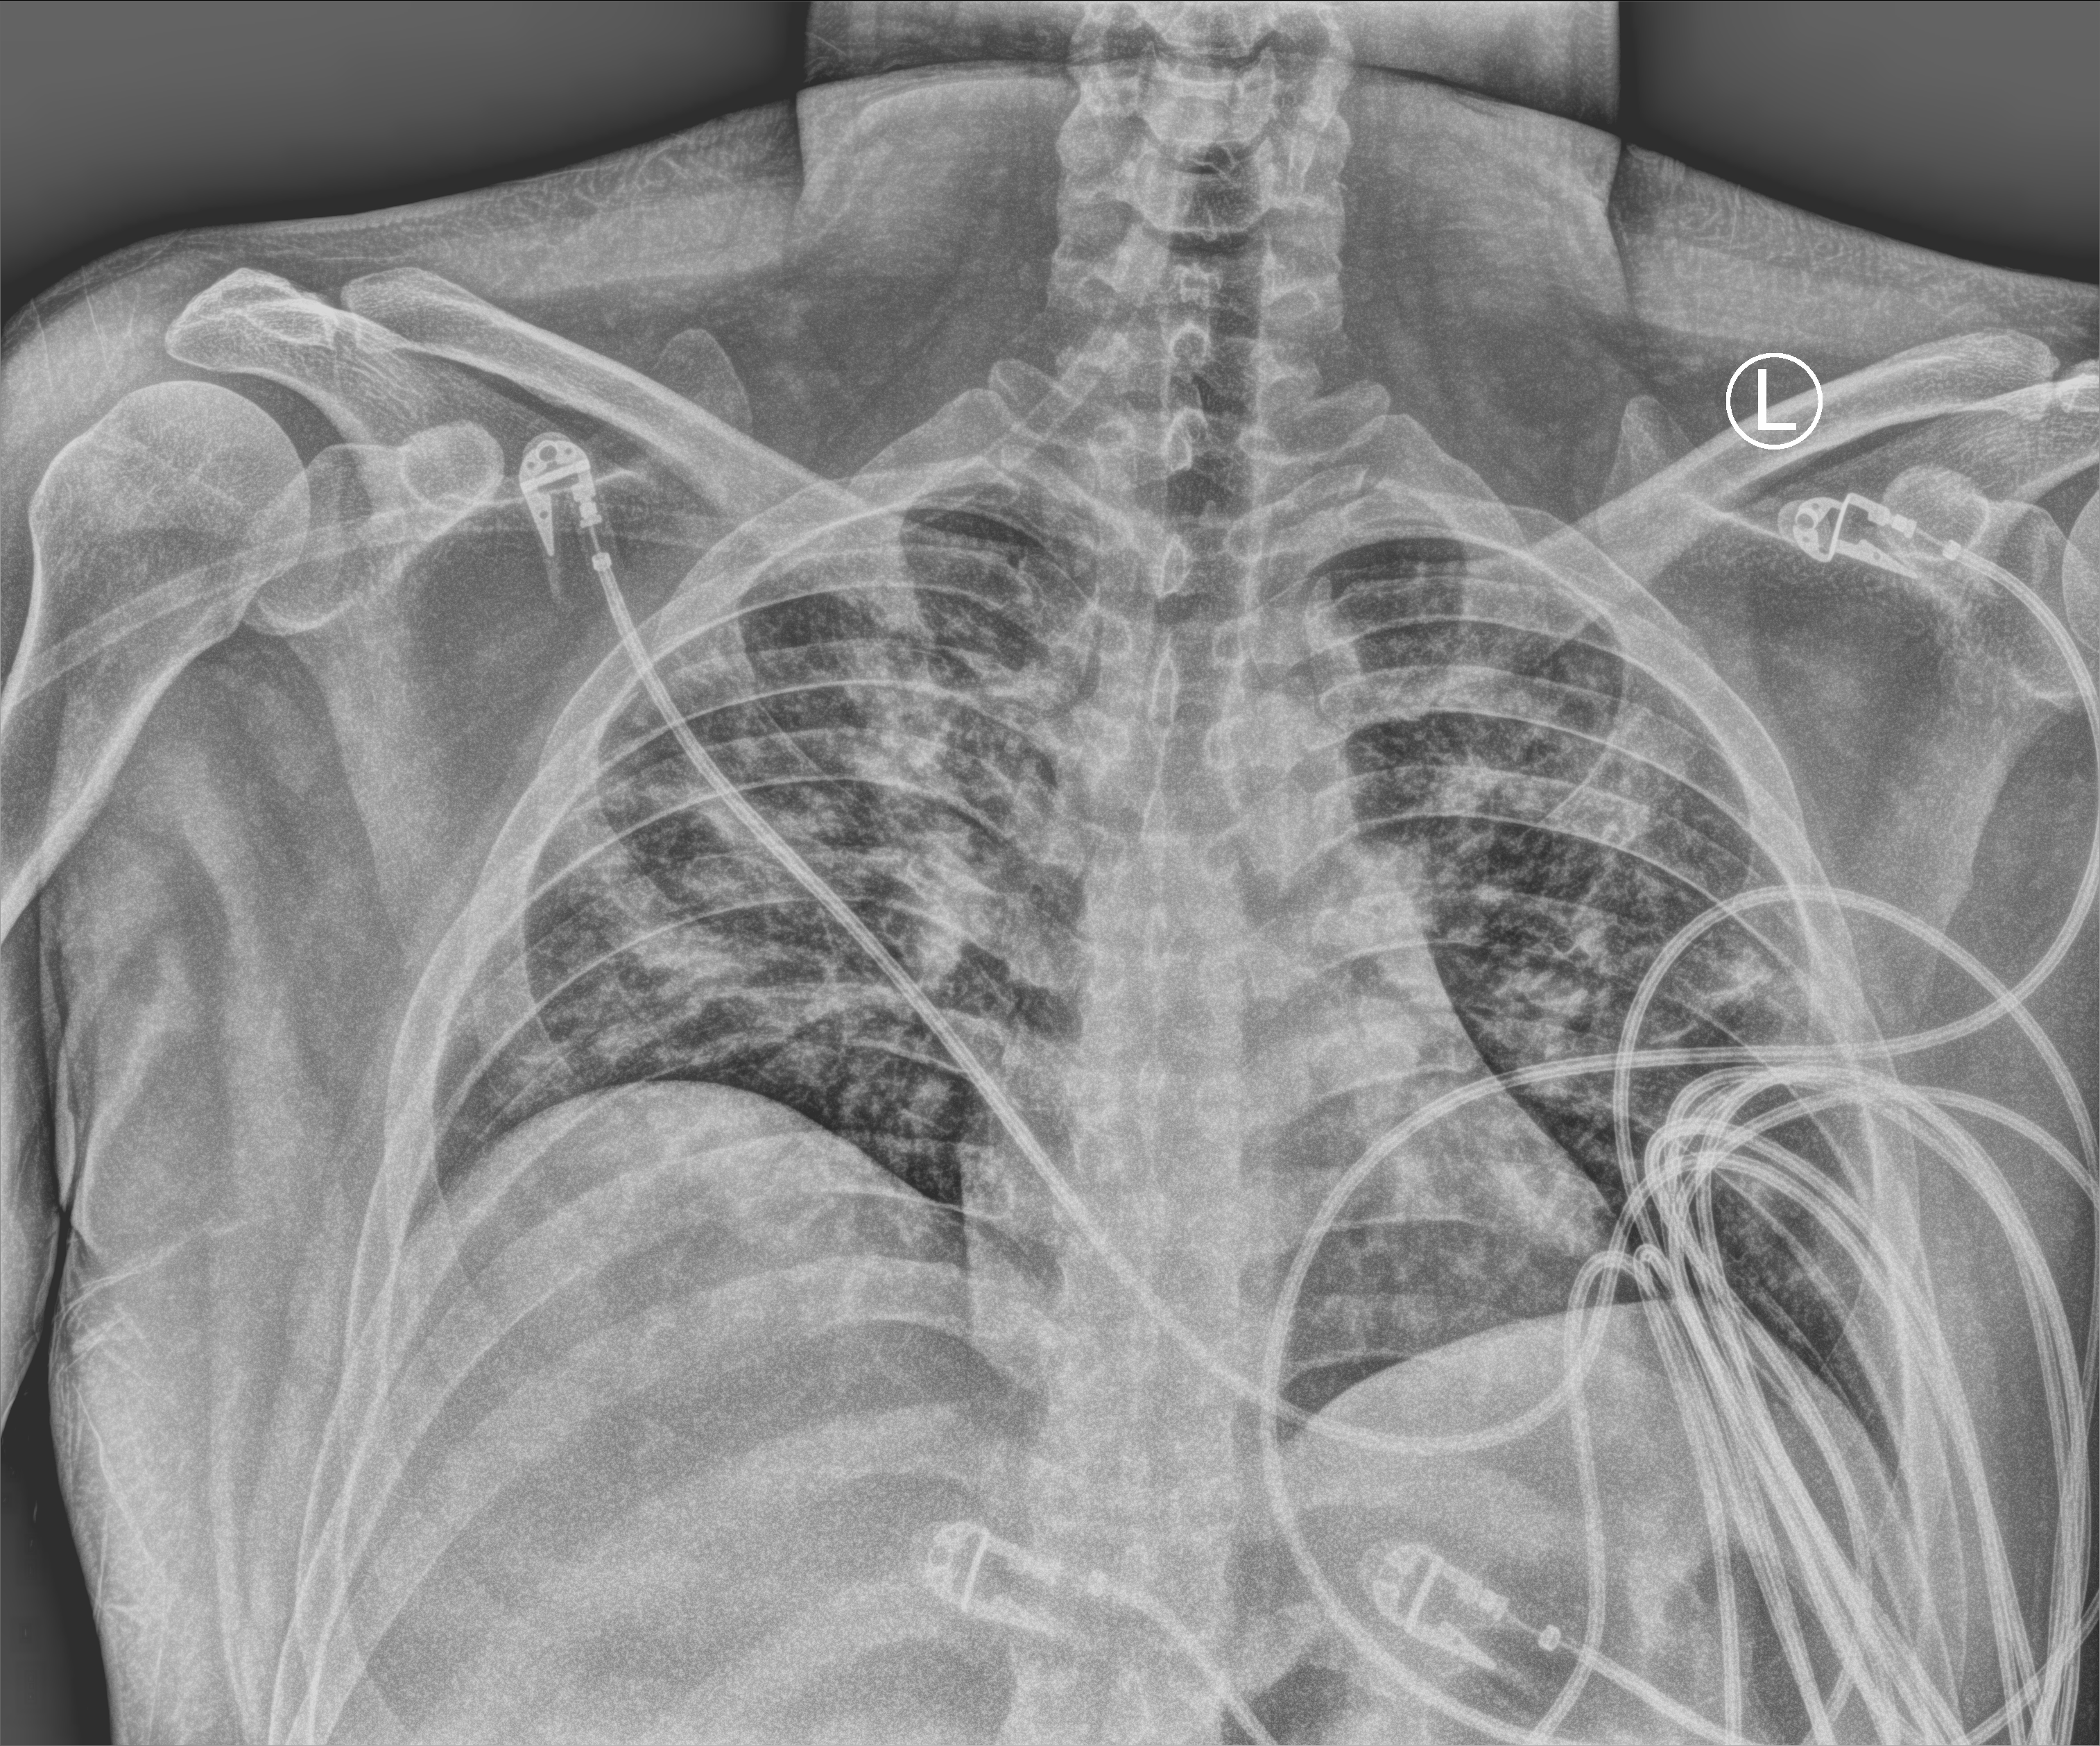
Chest X-ray (portable); anteroposterior (AP) projection. Patient hospitalised with COVID-19; male, aged 18–59 years.
From the hospital-stay record, not from the radiograph (when in the stay this image was taken is not recorded): COPD (admission record): no; mechanically ventilated during this hospital stay: yes; admitted to intensive care during this hospital stay: yes.